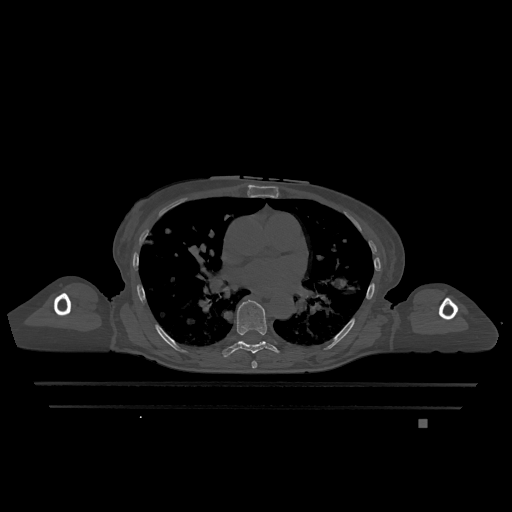
CT including the spine, one axial slice; position 739 of 1317 along the scan axis; bone window (W 1800 / L 400 HU); 512 × 512 image matrix, field of view 500 × 500 mm. Patient: female, 74 years. Case-level facts recorded for this patient, not image findings: primary cancer: lung.
Annotated regions visible in this slice (semi-automatic segmentation, software-assisted and operator-edited):
- T6 vertebra: bounding box <252,361,258,369> (left, top, right, bottom; pixels)
- T7 vertebra: <222,300,279,357>